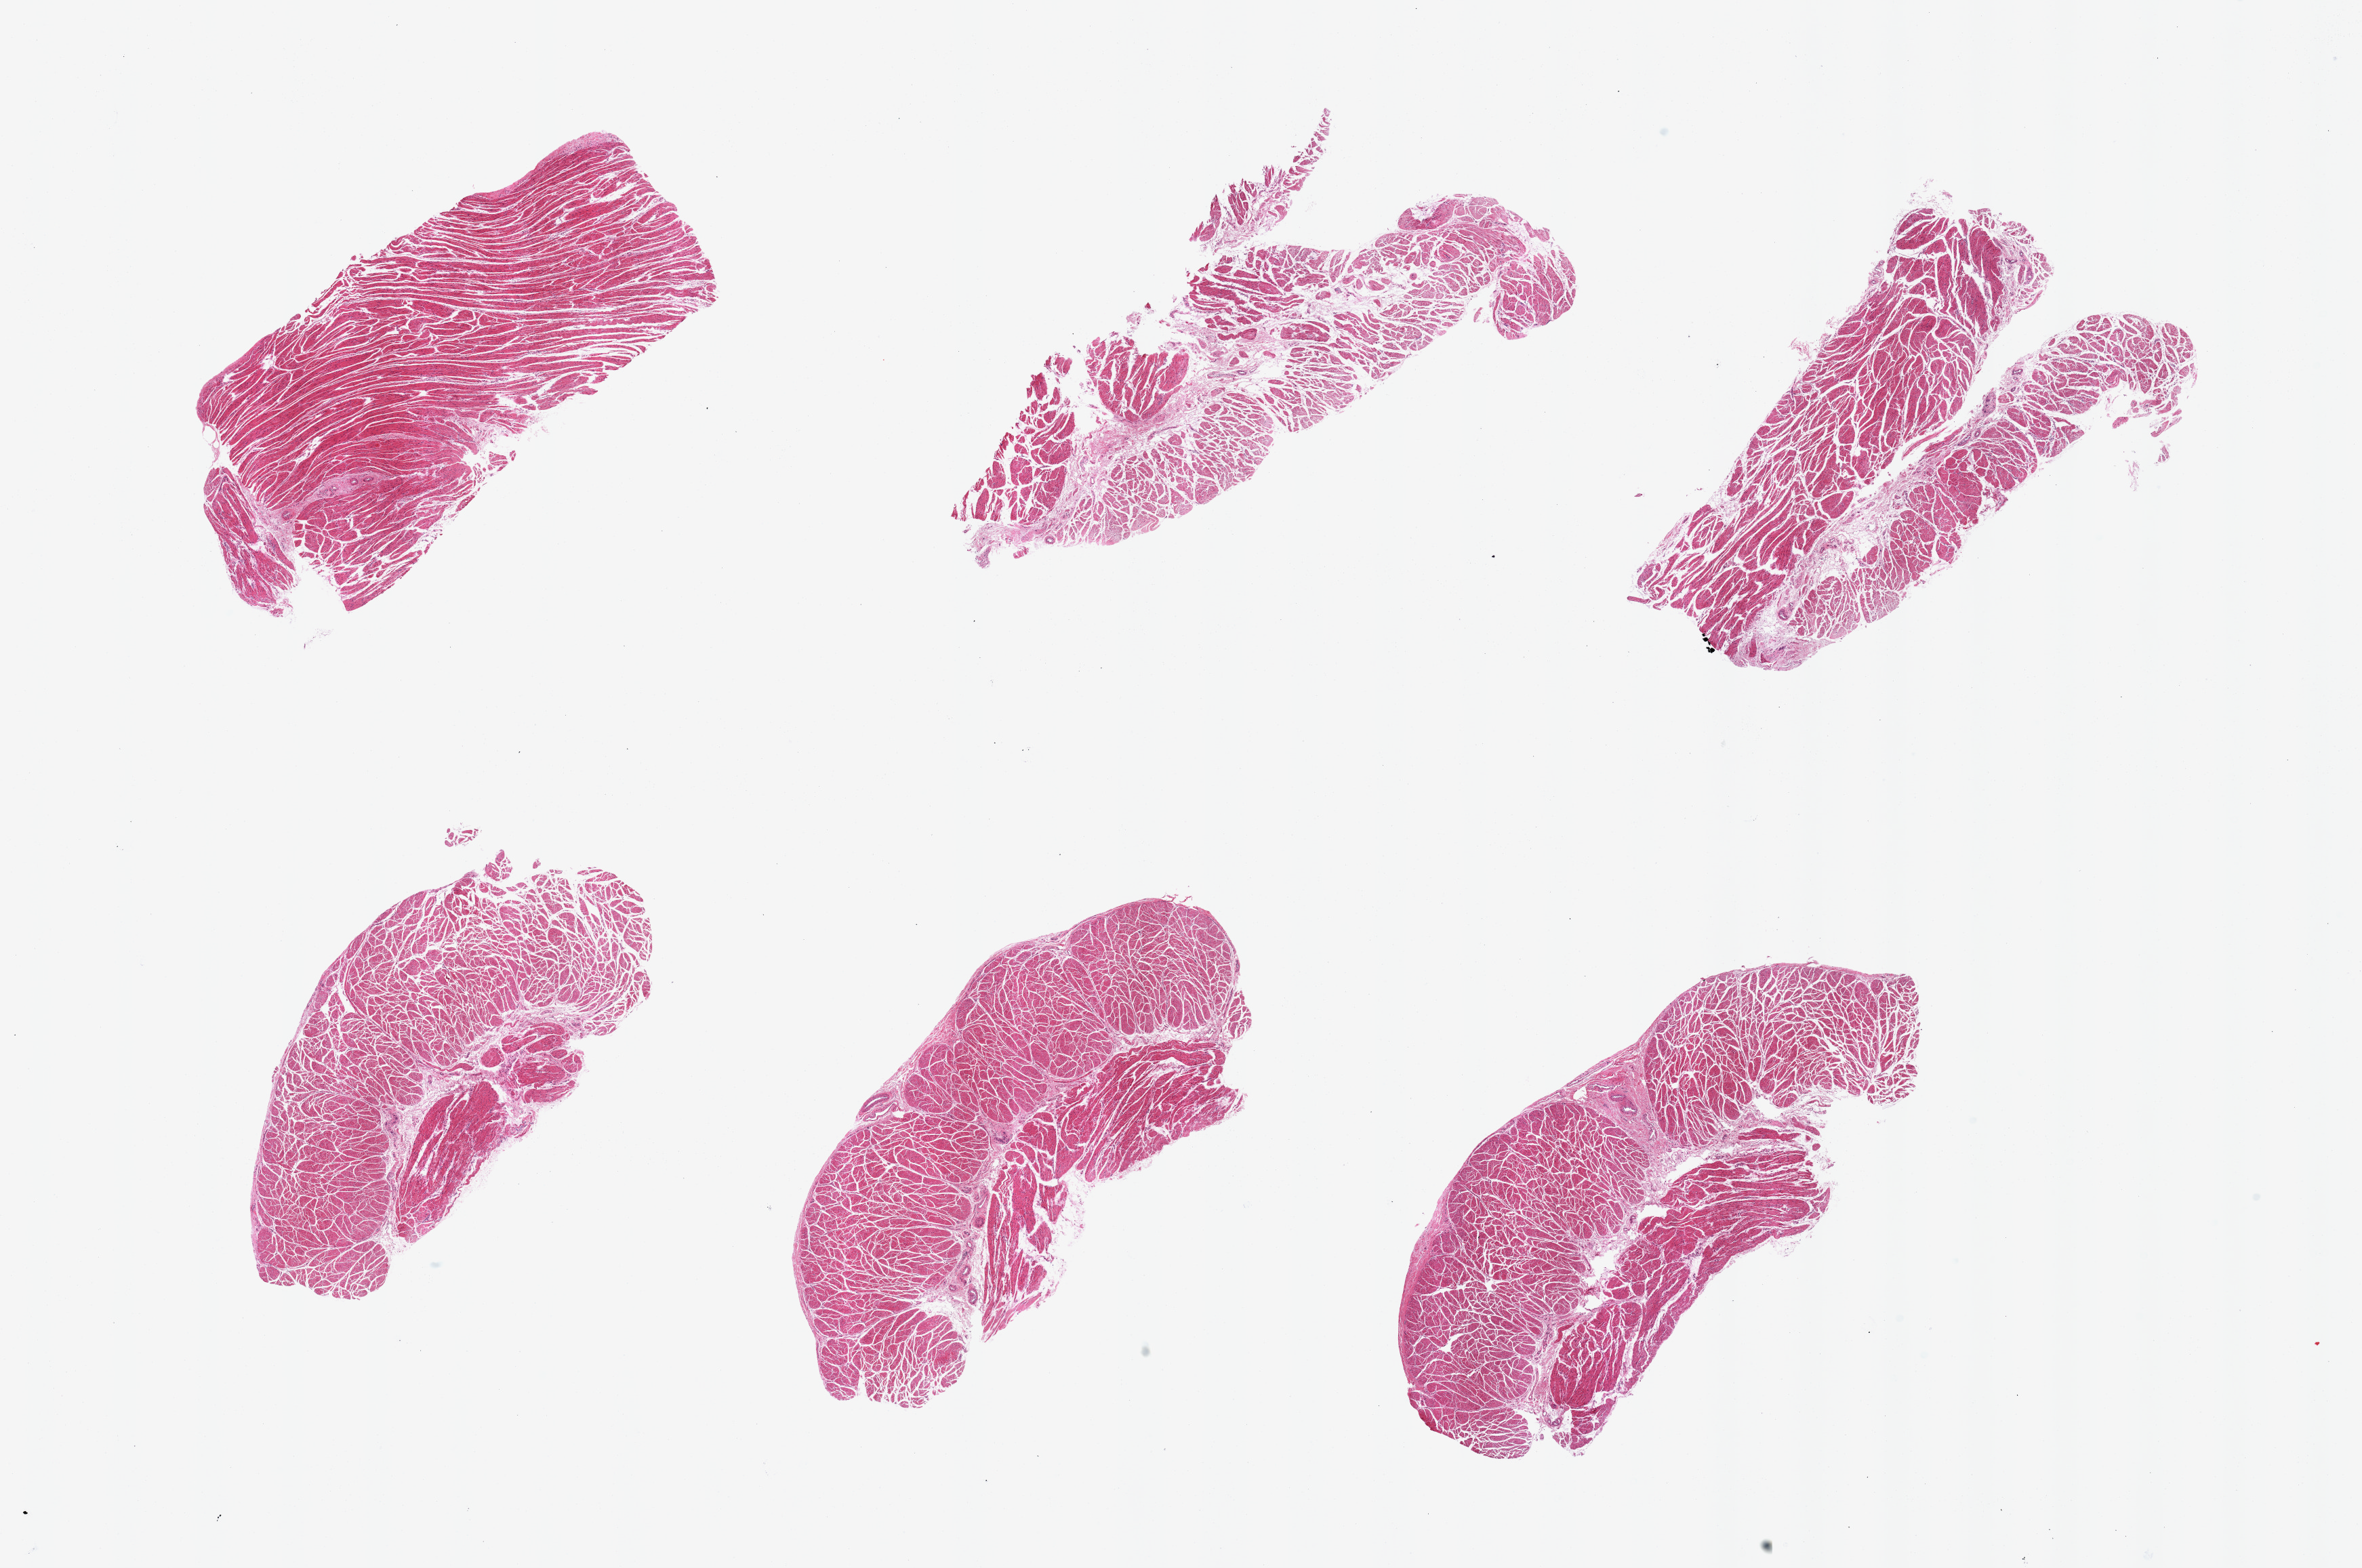
H&E whole-slide image, whole scanned area (about 27.6 x 18.3 mm) shown as a low-resolution overview. PAXgene-fixed, paraffin-embedded tissue. Section of esophageal muscle (target tissue). Donor tissue sample.
Pathologist's review note for this sample: 6 pieces, confirmed target muscularis.